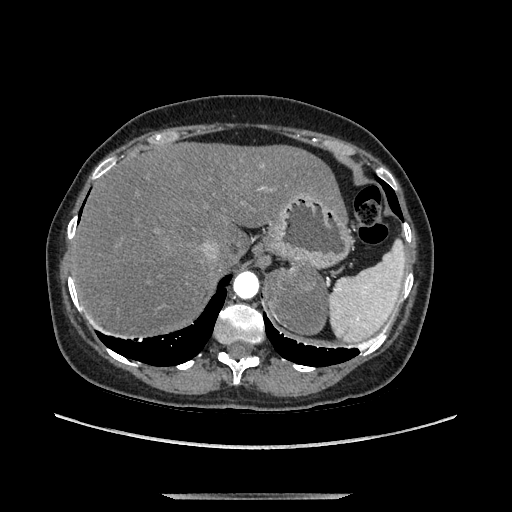
Contrast-enhanced abdominal CT, one axial slice; position 108 of 169 along the scan axis; soft-tissue window (W 400 / L 40 HU); 1.25 mm slice thickness; 512 × 512 image matrix, field of view 400 × 400 mm. Female patient. From the clinical record (not read from this slice): diagnosis: adrenocortical carcinoma; tumour side: left adrenal; tumour size at pathology: 9 cm; Ki-67 index: 2 %; stage (as recorded): 3.
Structures marked on this image (semi-automatic segmentation, software-assisted and operator-edited):
- mass: bounding box <269,269,326,333> (left, top, right, bottom; pixels)